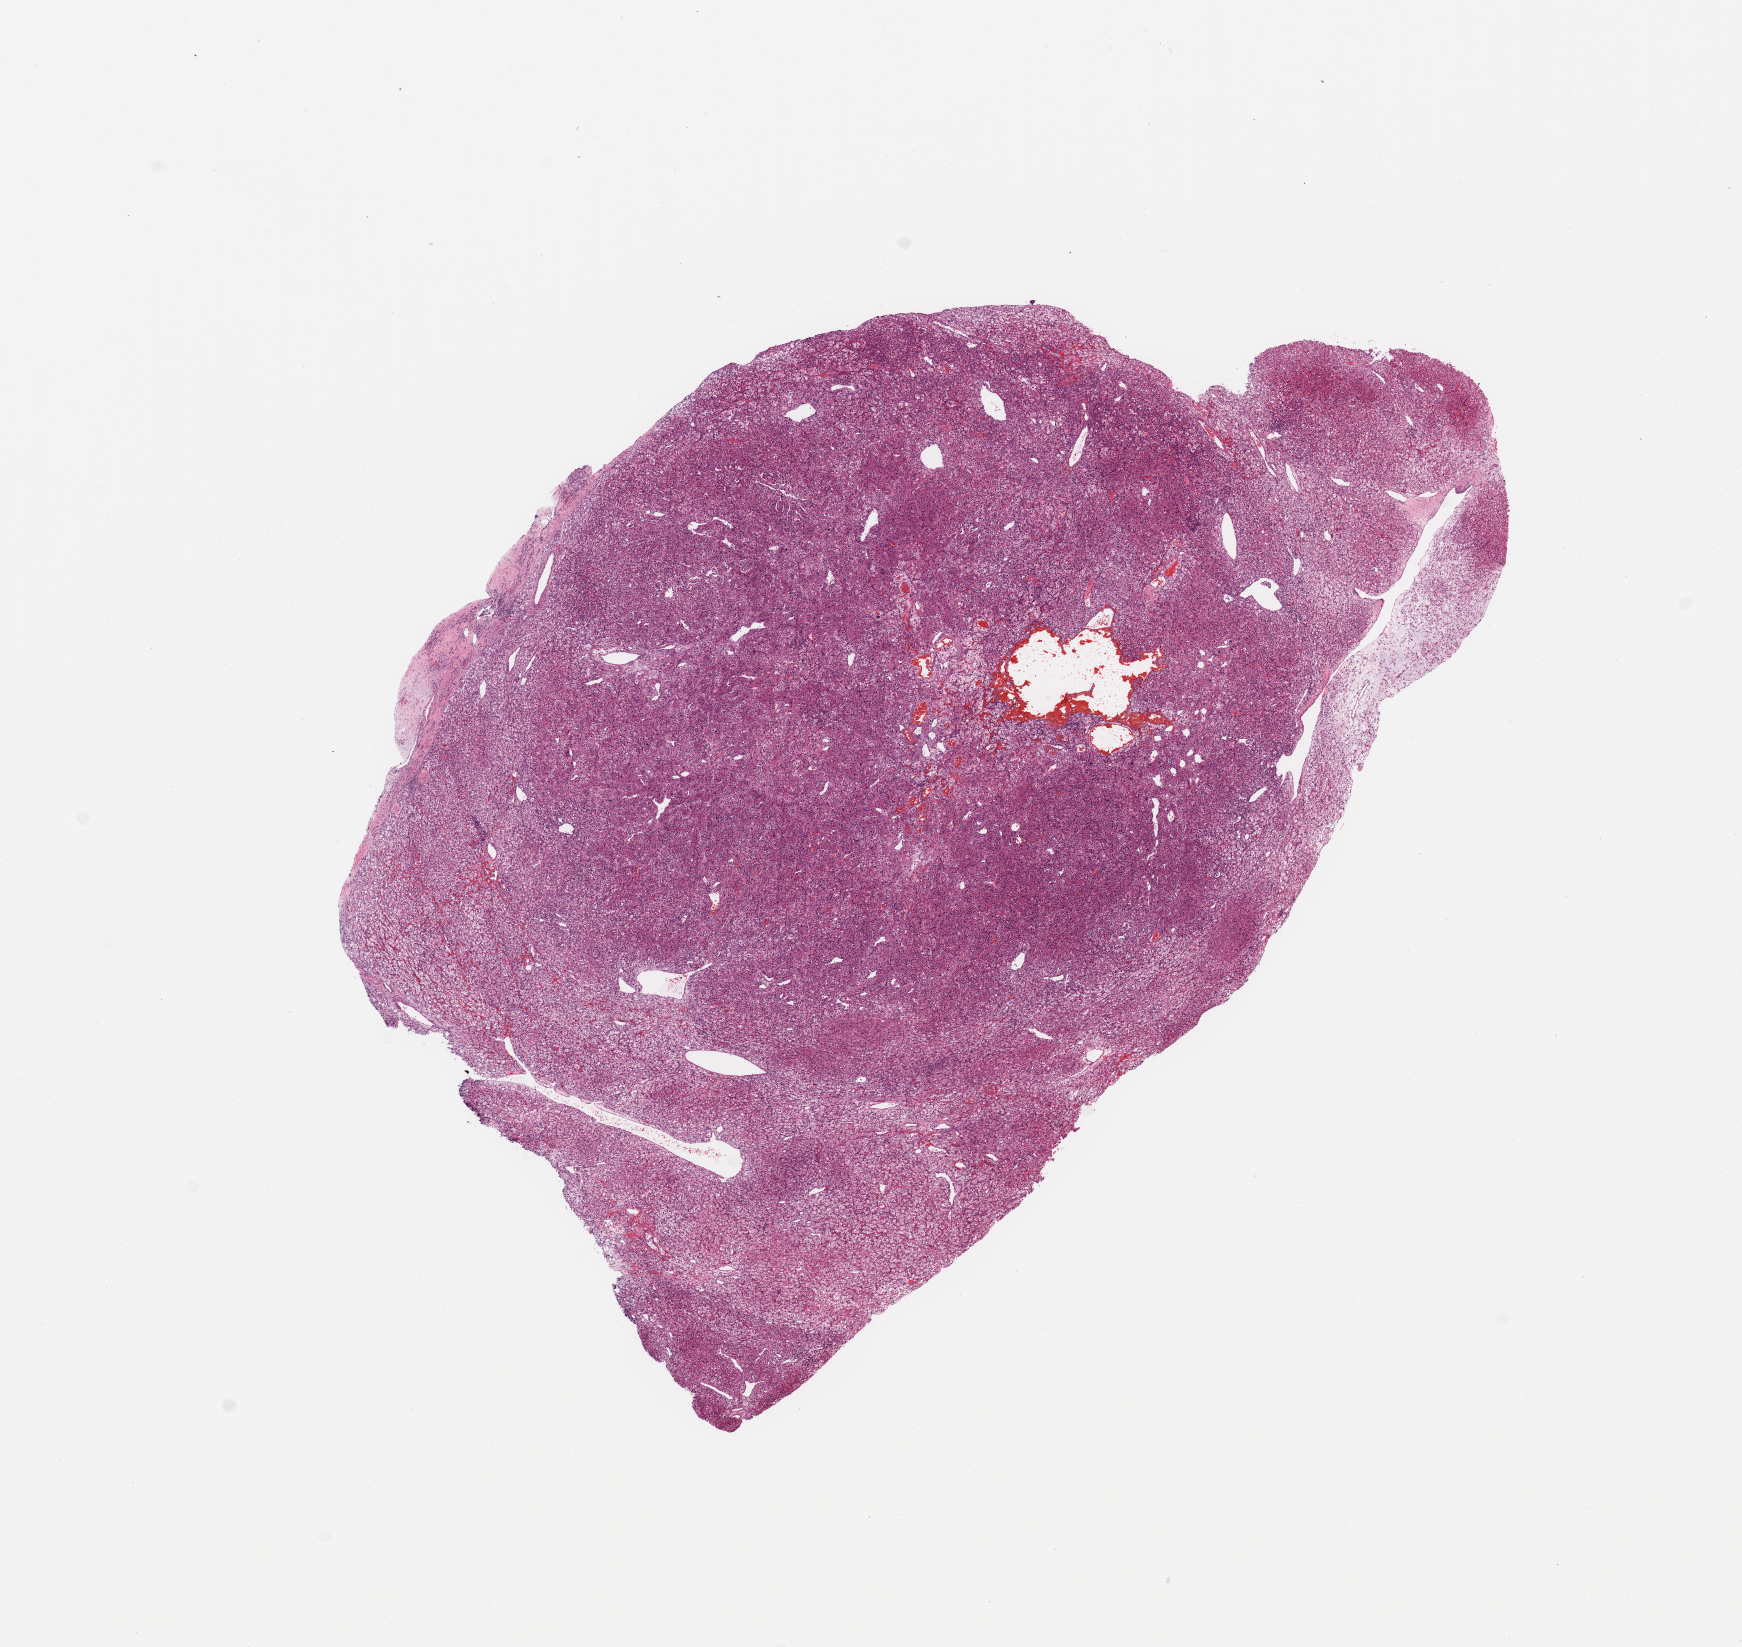
Hematoxylin and eosin (H&E) stained whole-slide image, low-resolution overview of the scanned area, about 13.8 x 13.0 mm (slide scanned at 20x), tumour tissue sample, sampled site: kidney. 47-year-old male patient. Histologic grade: G3 (poorly differentiated). Composition of this section per pathologist review: tumour nuclei 95%, necrosis 0%.
* histologic diagnosis: Renal cell carcinoma, NOS
* primary tumour site (as recorded): upper pole
* AJCC pathologic stage: I